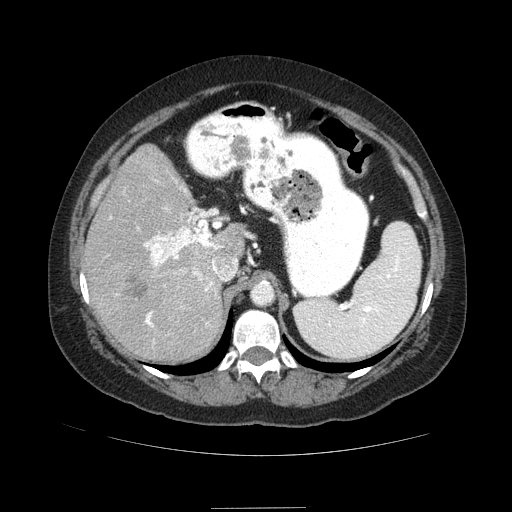
Contrast-enhanced abdominal CT (liver protocol), one axial slice; position 56 of 89 along the scan axis; reconstruction kernel STANDARD; soft-tissue window (W 400 / L 40 HU); 2.5 mm slice thickness; 512 × 512 image matrix. Case-level facts recorded for this patient, not image findings: diagnosis: hepatocellular carcinoma (patient treated with transarterial chemoembolisation; whether this scan precedes or follows treatment is not stated here); TNM stage (as recorded): Stage-IIIB; Child-Pugh class: A; tumour nodularity: multinodular.
Annotated regions visible in this slice (semi-automatically segmented with operator editing):
- liver parenchyma outside the tumour (the mass and vessels are separate outlines, so this box may not span the whole liver): bounding box (x1, y1, x2, y2) in pixels: (82, 144, 246, 362)
- mass: (117, 272, 147, 305)
- liver vessels: (110, 180, 223, 327)